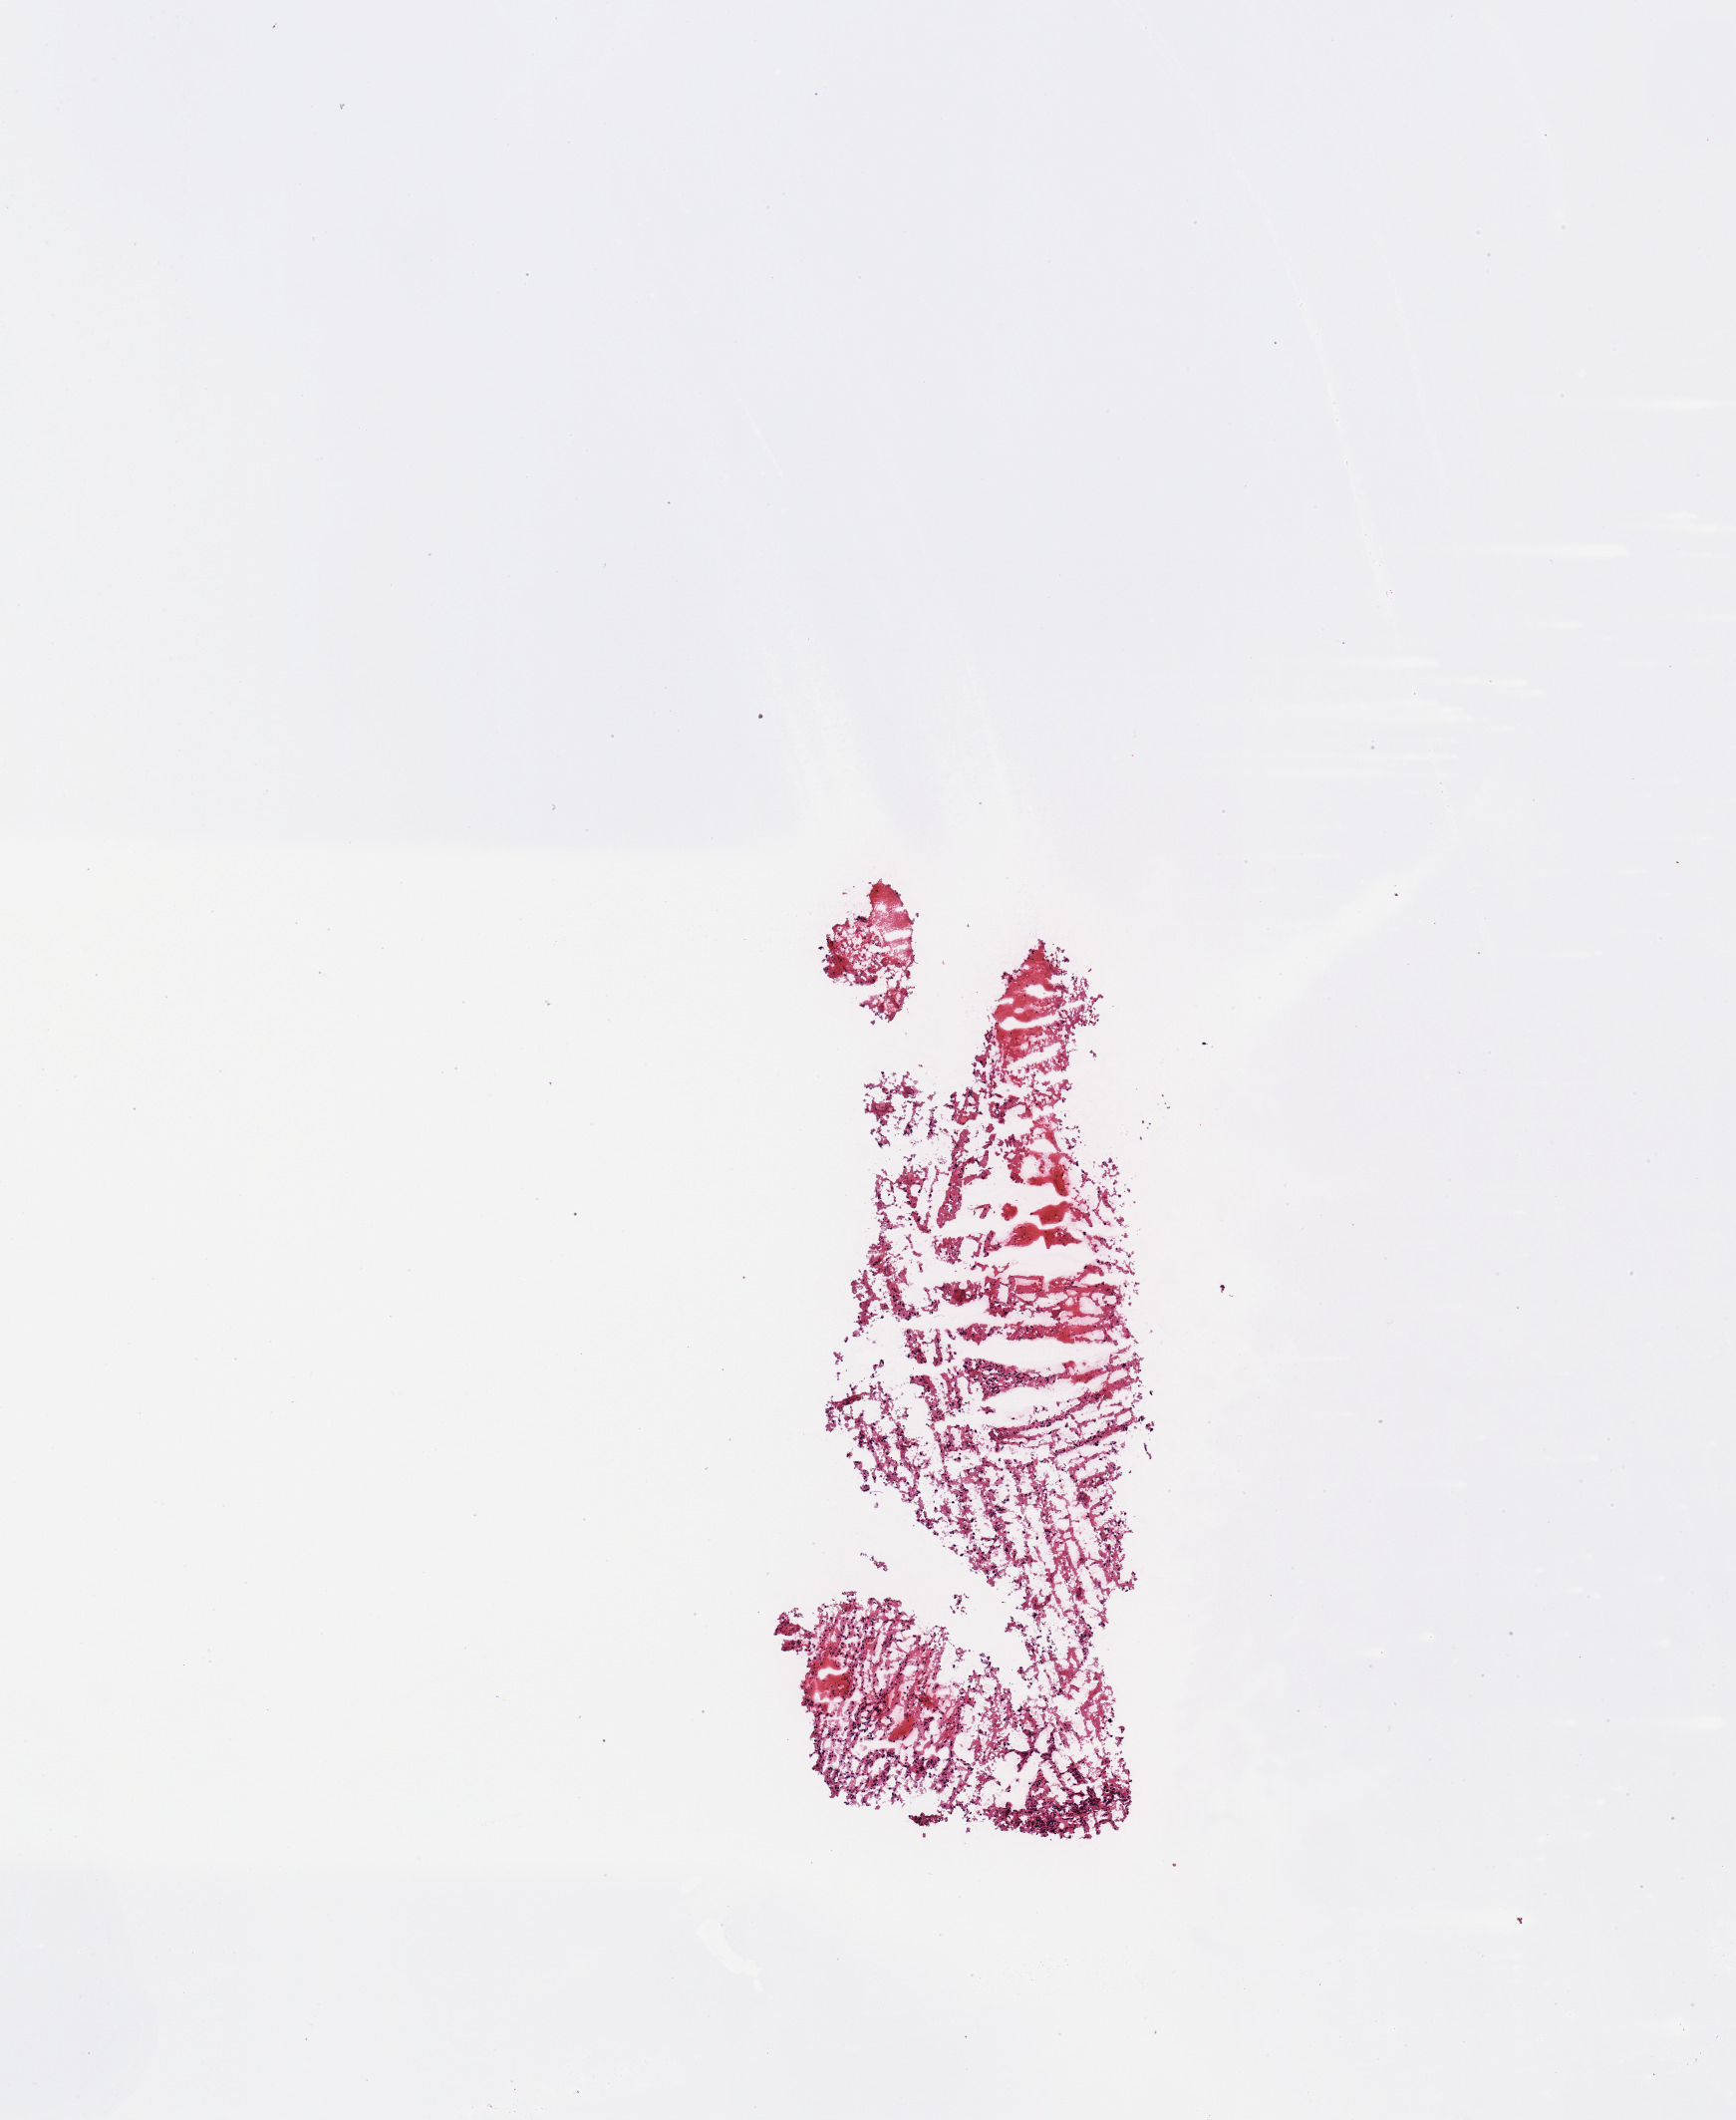
Whole-slide histology image, Hematoxylin and eosin (H&E) stained — whole scanned area (about 6.9 x 8.4 mm) shown as a low-resolution overview. Brain, tissue type not recorded.
Patient diagnosis (cohort enrolment): glioblastoma multiforme (brain).